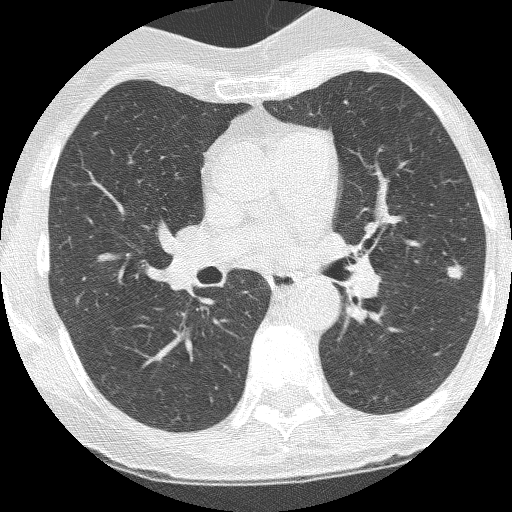
Low-dose screening chest CT, axial slice, third annual screen, lung window (W 1500 / L -600 HU), lung (sharp) reconstruction kernel (BONE), slice 150 of 247 in the series. Female participant, aged 60 years at enrolment. Current smoker at enrolment.
Lesion marked by an expert reader, box from (x=435, y=257) to (x=472, y=293) px. The screening reader recorded 2 non-calcified nodules or masses ≥4 mm on this exam (left upper lobe, left upper lobe); which of them this box marks is not recorded. Official screen result: positive, other.